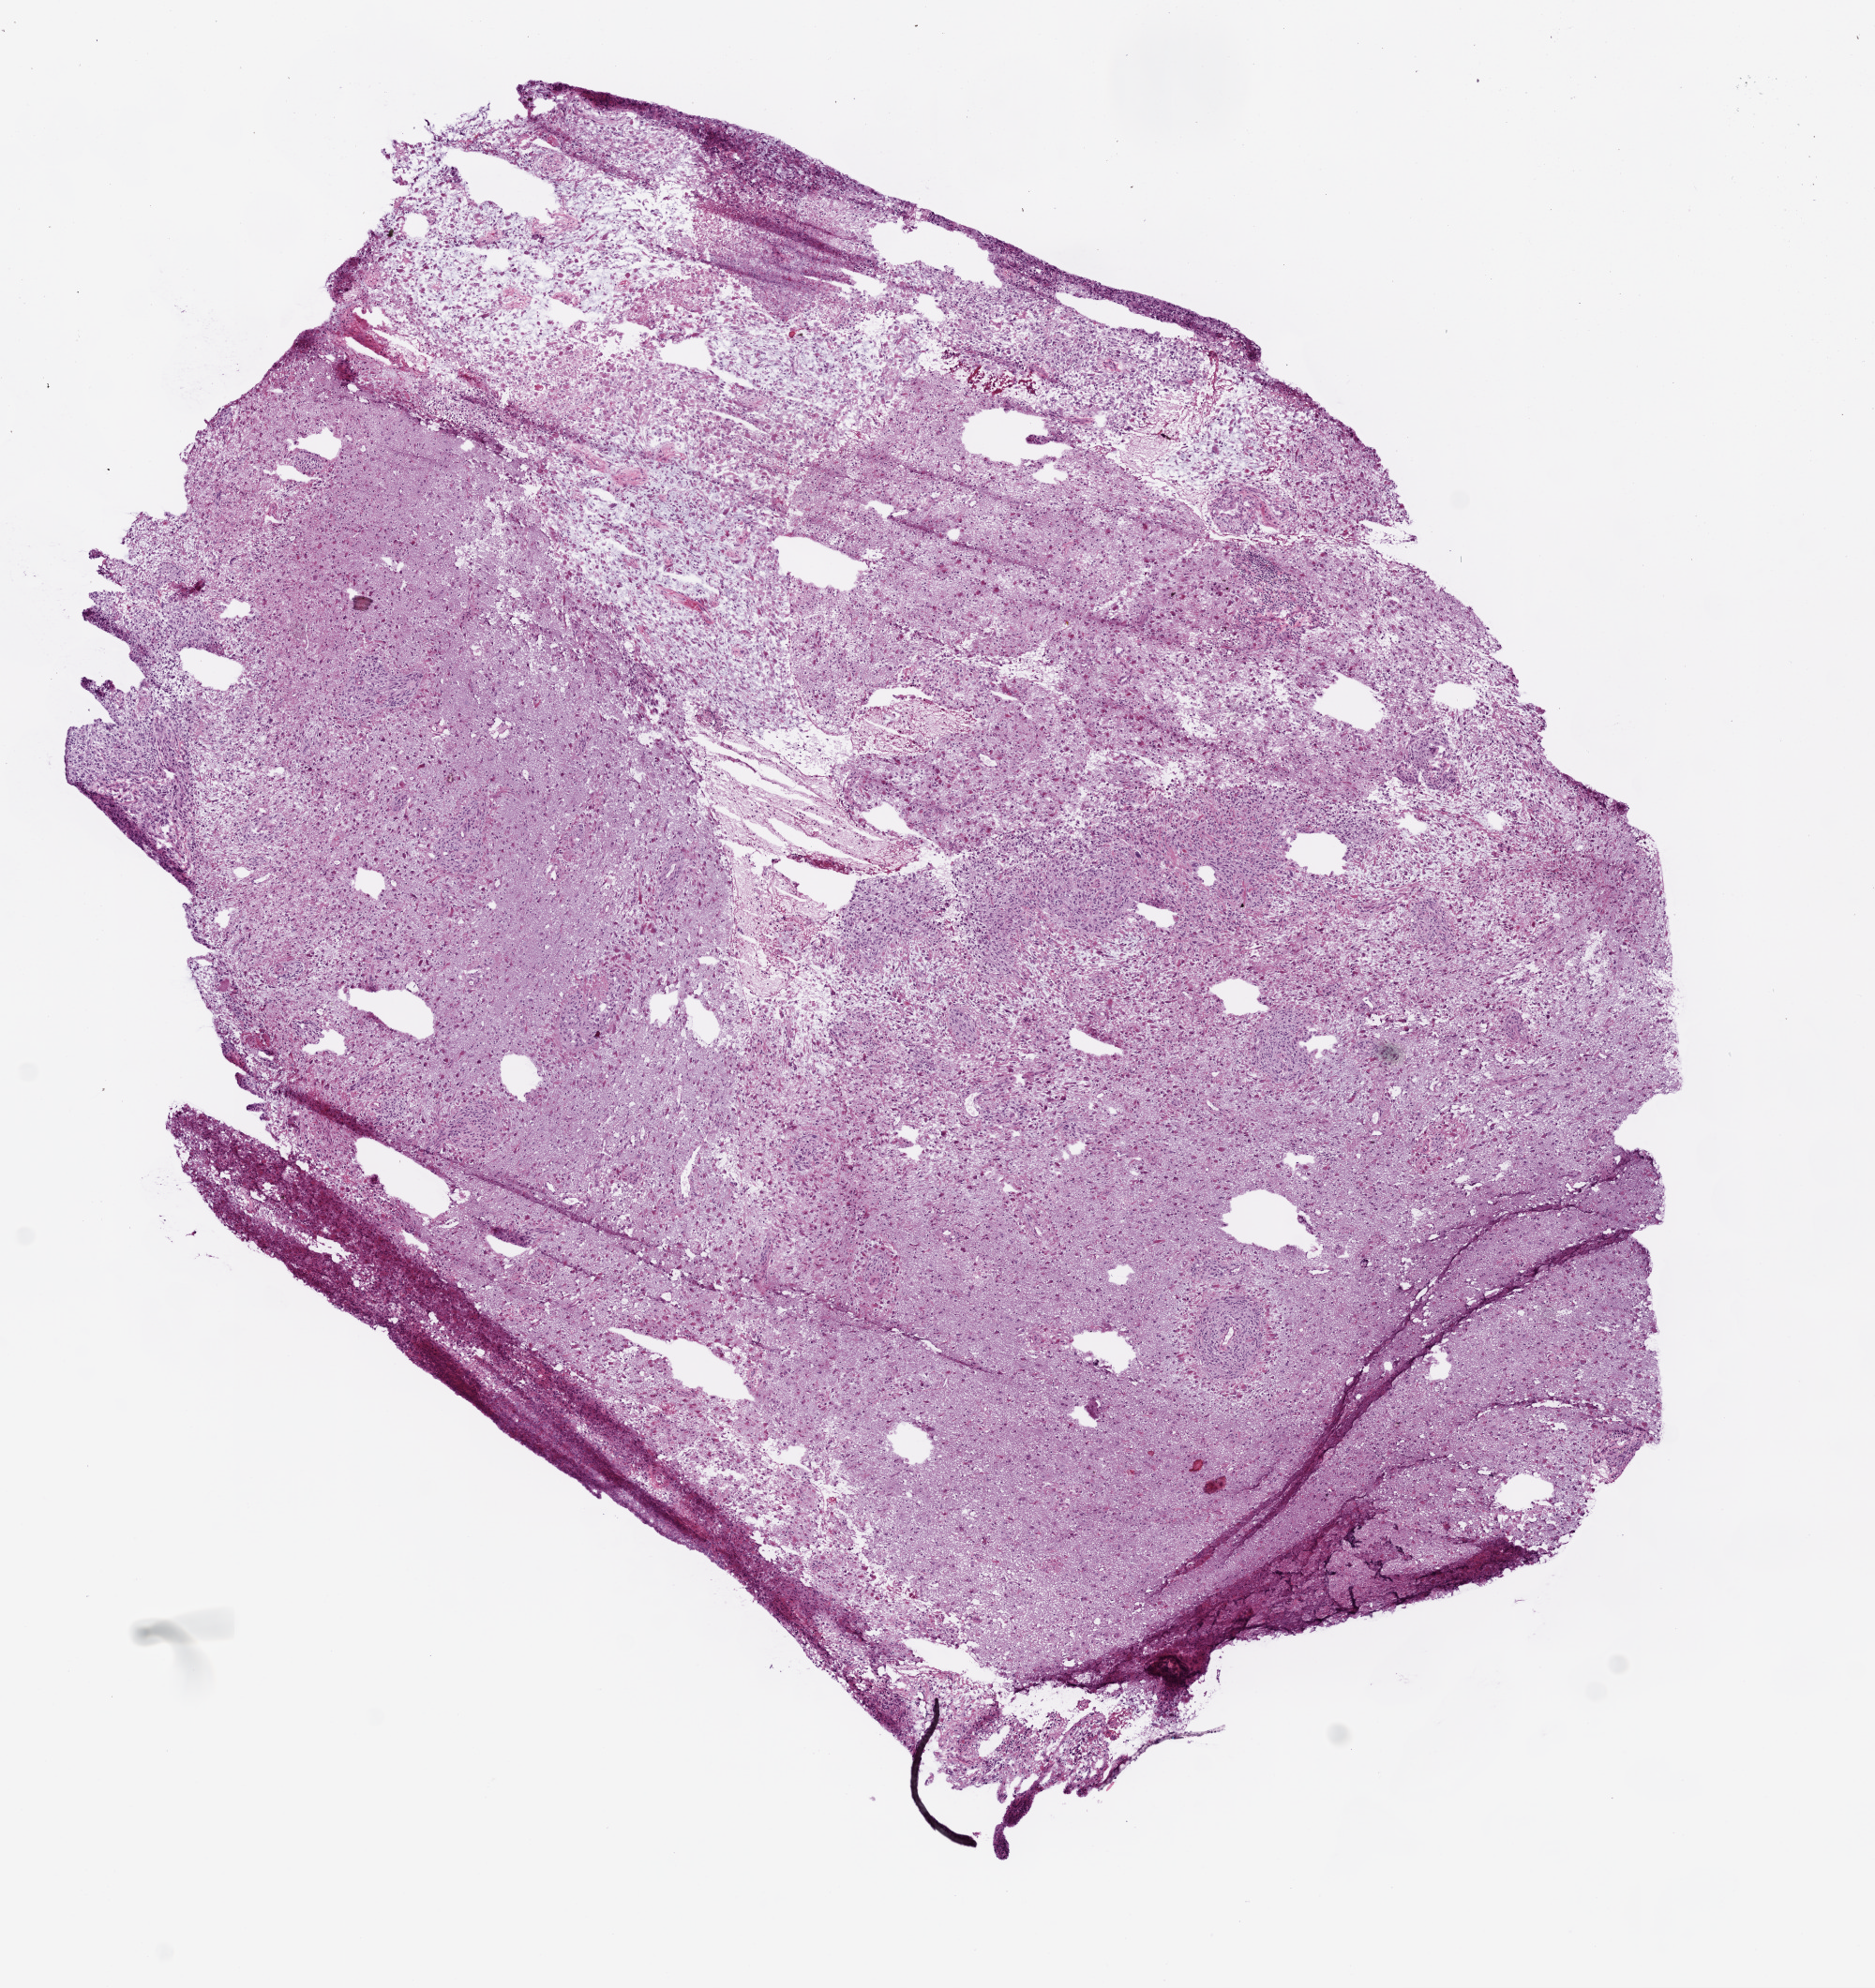
H&E-stained whole-slide image, a low-resolution overview of the entire scanned area, about 8.0 x 8.5 mm (from a 20x scan); frozen section from the top of the tissue portion; sample: primary tumour, brain. Female, age 63 years at initial diagnosis.
Histologic diagnosis: Glioblastoma.